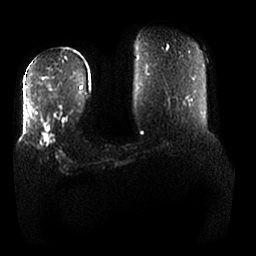
Breast MRI, one axial slice; position 7 of 25 along the scan axis; diffusion-weighted series; image 2 of 4 stored at this slice position (different b-values; order by instance number); 1.5 T; 4 mm slice thickness; 256 × 256 image matrix. Female patient.
Annotated regions visible in this slice (manually delineated by an expert):
- tumour on diffusion-weighted imaging: bounding box (x1, y1, x2, y2) in pixels: (41, 133, 53, 145)